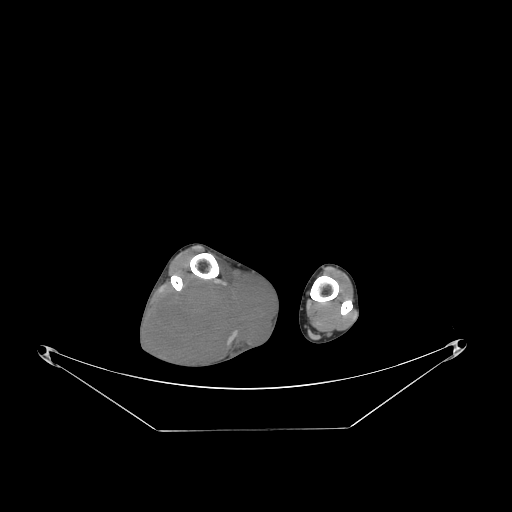
CT of an extremity soft-tissue mass (from a PET/CT study), one axial slice; position 64 of 267 along the scan axis; 140 kVp; soft-tissue window (W 400 / L 40 HU); 3.75 mm slice thickness; 512 × 512 image matrix, field of view 500 × 500 mm. Male patient. From the clinical record (not read from this slice): histological type: liposarcoma - round cell; grade: high; site of the primary tumour: right calf.
Annotated regions visible in this slice (expert contour drawn on MRI and transferred to this co-registered scan by the dataset authors):
- gross tumour volume (mass): bounding box <151,270,277,369> (left, top, right, bottom; pixels)